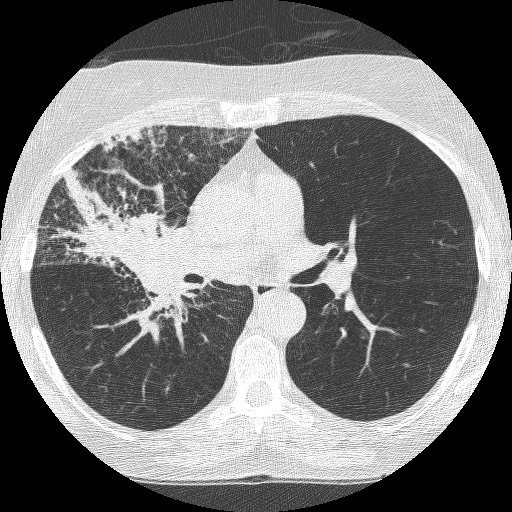
Axial slice from a low-dose chest CT screening exam, third screening round (two years after baseline), lung window (W 1500 / L -600 HU), 512 × 512 image matrix, field of view 294 × 294 mm. Female, age 64 years at enrolment. Former smoker at enrolment.
- Expert-annotated lung lesion, box from (x=67, y=182) to (x=201, y=318) px.
- Reader record for this screening exam (exam-level; its link to the box is not recorded): non-calcified nodule or mass ≥4 mm, right upper lobe, 49 × 43 mm, spiculated (stellate) margins, soft tissue attenuation, pre-existing on the prior screen: yes; interval growth: yes.
- Official screen result: positive, other.
- Participant outcome: lung cancer diagnosed 7 days after this screen — adenocarcinoma, NOS, right upper lobe, right middle lobe, right hilum, stage IV (AJCC 6th edition), 85 mm at pathology.